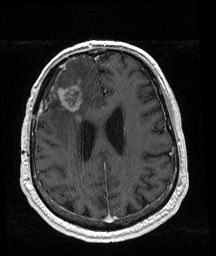
Brain MRI from a brain-tumour surgery series, one axial slice. T1-weighted post-contrast. 1 mm slice thickness. 216 × 256 image matrix, field of view 211 × 250 mm. Case-level facts recorded for this patient, not image findings: histopathology: Glioblastoma; WHO grade: 4; IDH mutation: no; tumour location: Right Frontal.
Outlined on this slice (expert manual segmentation):
- tumour: bounding box [x1, y1, x2, y2] px = [39, 85, 91, 112]